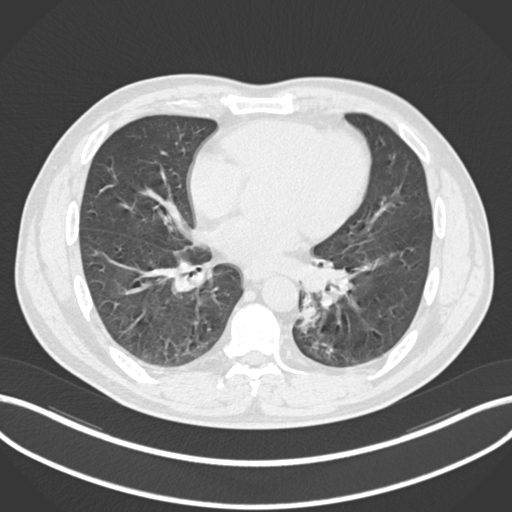
Chest CT, one axial slice; position 94 of 223 along the scan axis; reconstruction kernel B30f; lung window (W 1500 / L -600 HU); 1 mm slice thickness; 512 × 512 image matrix. Male patient, age 50 years. Case-level facts recorded for this patient, not image findings: clinical TNM (as recorded): T2a N3 M0.
Outlined on this slice (rectangle marked by the reading radiologist):
- lung tumour (recorded histology: squamous cell carcinoma): bounding box (x1, y1, x2, y2) in pixels: (293, 299, 322, 335)